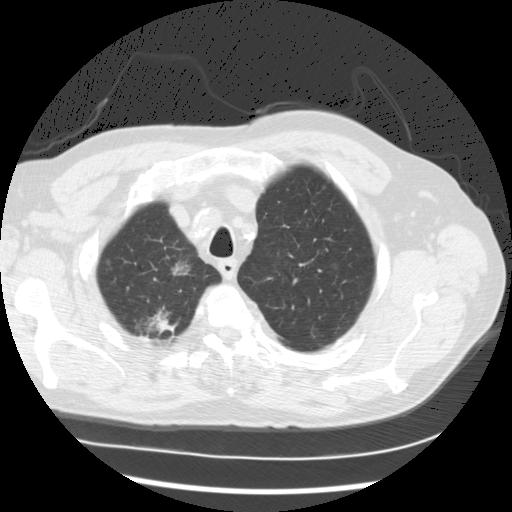
Axial slice from a low-dose chest CT screening exam. Baseline annual screen. Lung window (W 1500 / L -600 HU). 120 kVp. Slice 25 of 122 in the series. 512 × 512 image matrix. Male participant, aged 68 years at enrolment. Current smoker at enrolment.
Lesion marked by an expert reader, box from (x=115, y=289) to (x=192, y=361) px. The screening reader recorded 3 non-calcified nodules or masses ≥4 mm on this exam (right upper lobe, right upper lobe, right lower lobe); which of them this box marks is not recorded. Official screen result: positive, change unspecified: nodule(s) >= 4 mm or enlarging nodule(s), mass(es), or other non-specific abnormalities suspicious for lung cancer. Later outcome: lung cancer diagnosed 90 days after this screen — adenocarcinoma, NOS, right upper lobe, right lower lobe, well differentiated (G1), stage IV (AJCC 6th edition), 35 mm at pathology.